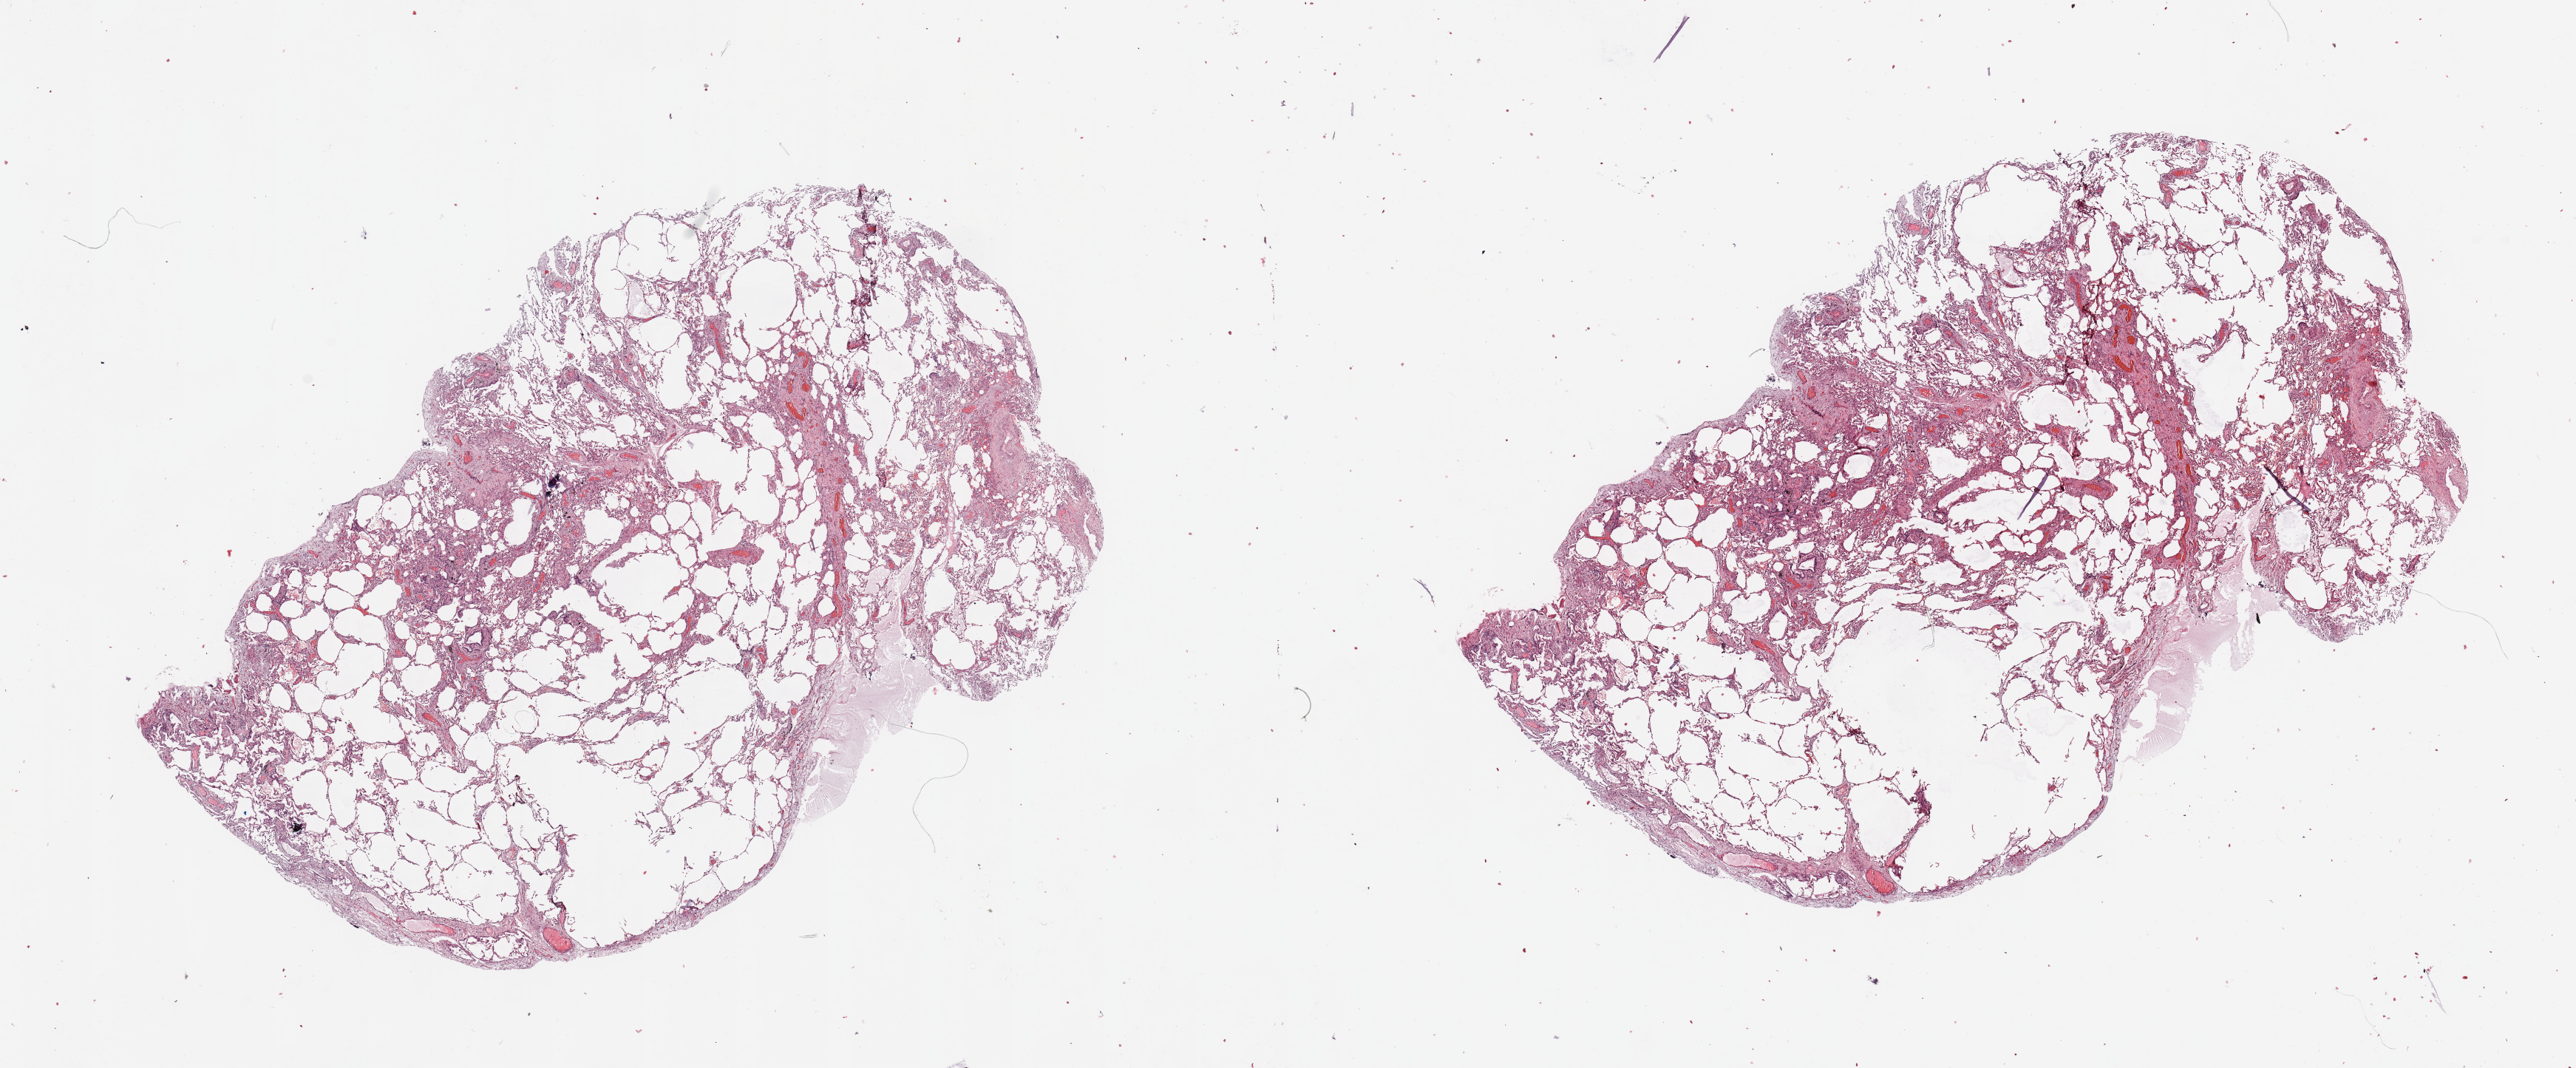
Whole-slide histology image, H&E-stained, a low-resolution overview of the entire scanned area, about 27.6 x 11.4 mm; lung, normal (non-tumour) tissue. Male, 61 y/o.
This section: normal (non-tumour) tissue from the same patient. Patient diagnosis: Squamous cell carcinoma, NOS.